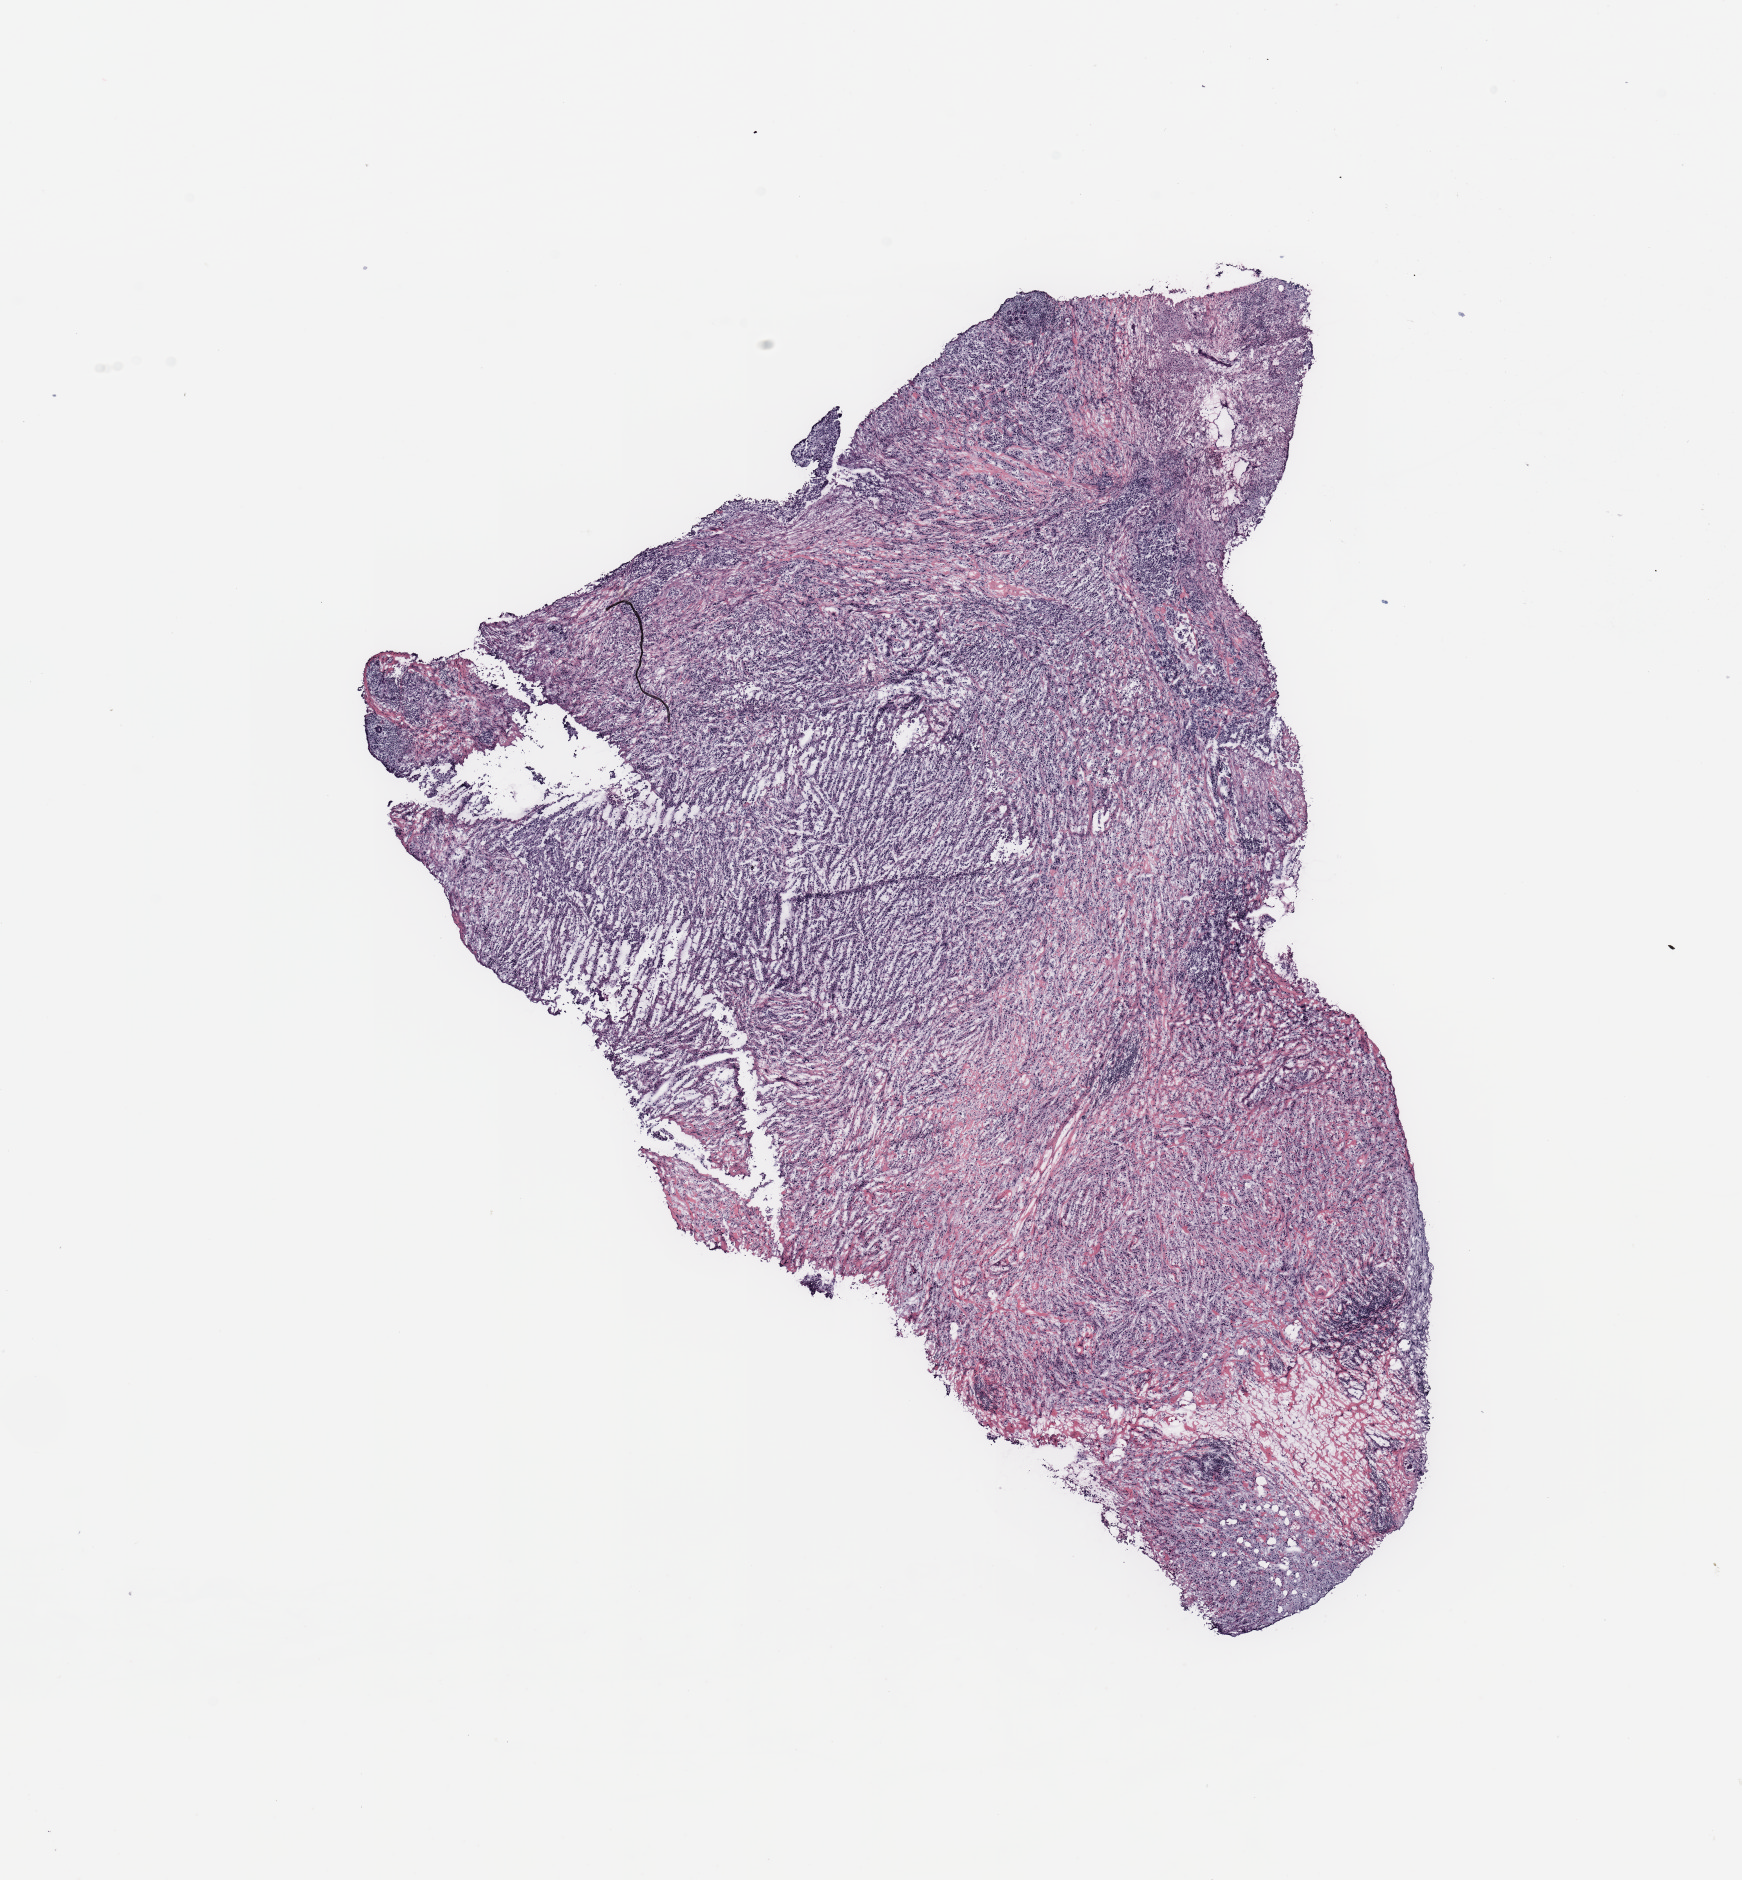
H&E whole-slide image — whole scanned area (about 13.8 x 14.9 mm) shown as a low-resolution overview; breast, tissue type not recorded. Female, 49 y/o.
• patient diagnosis: Infiltrating duct carcinoma, NOS